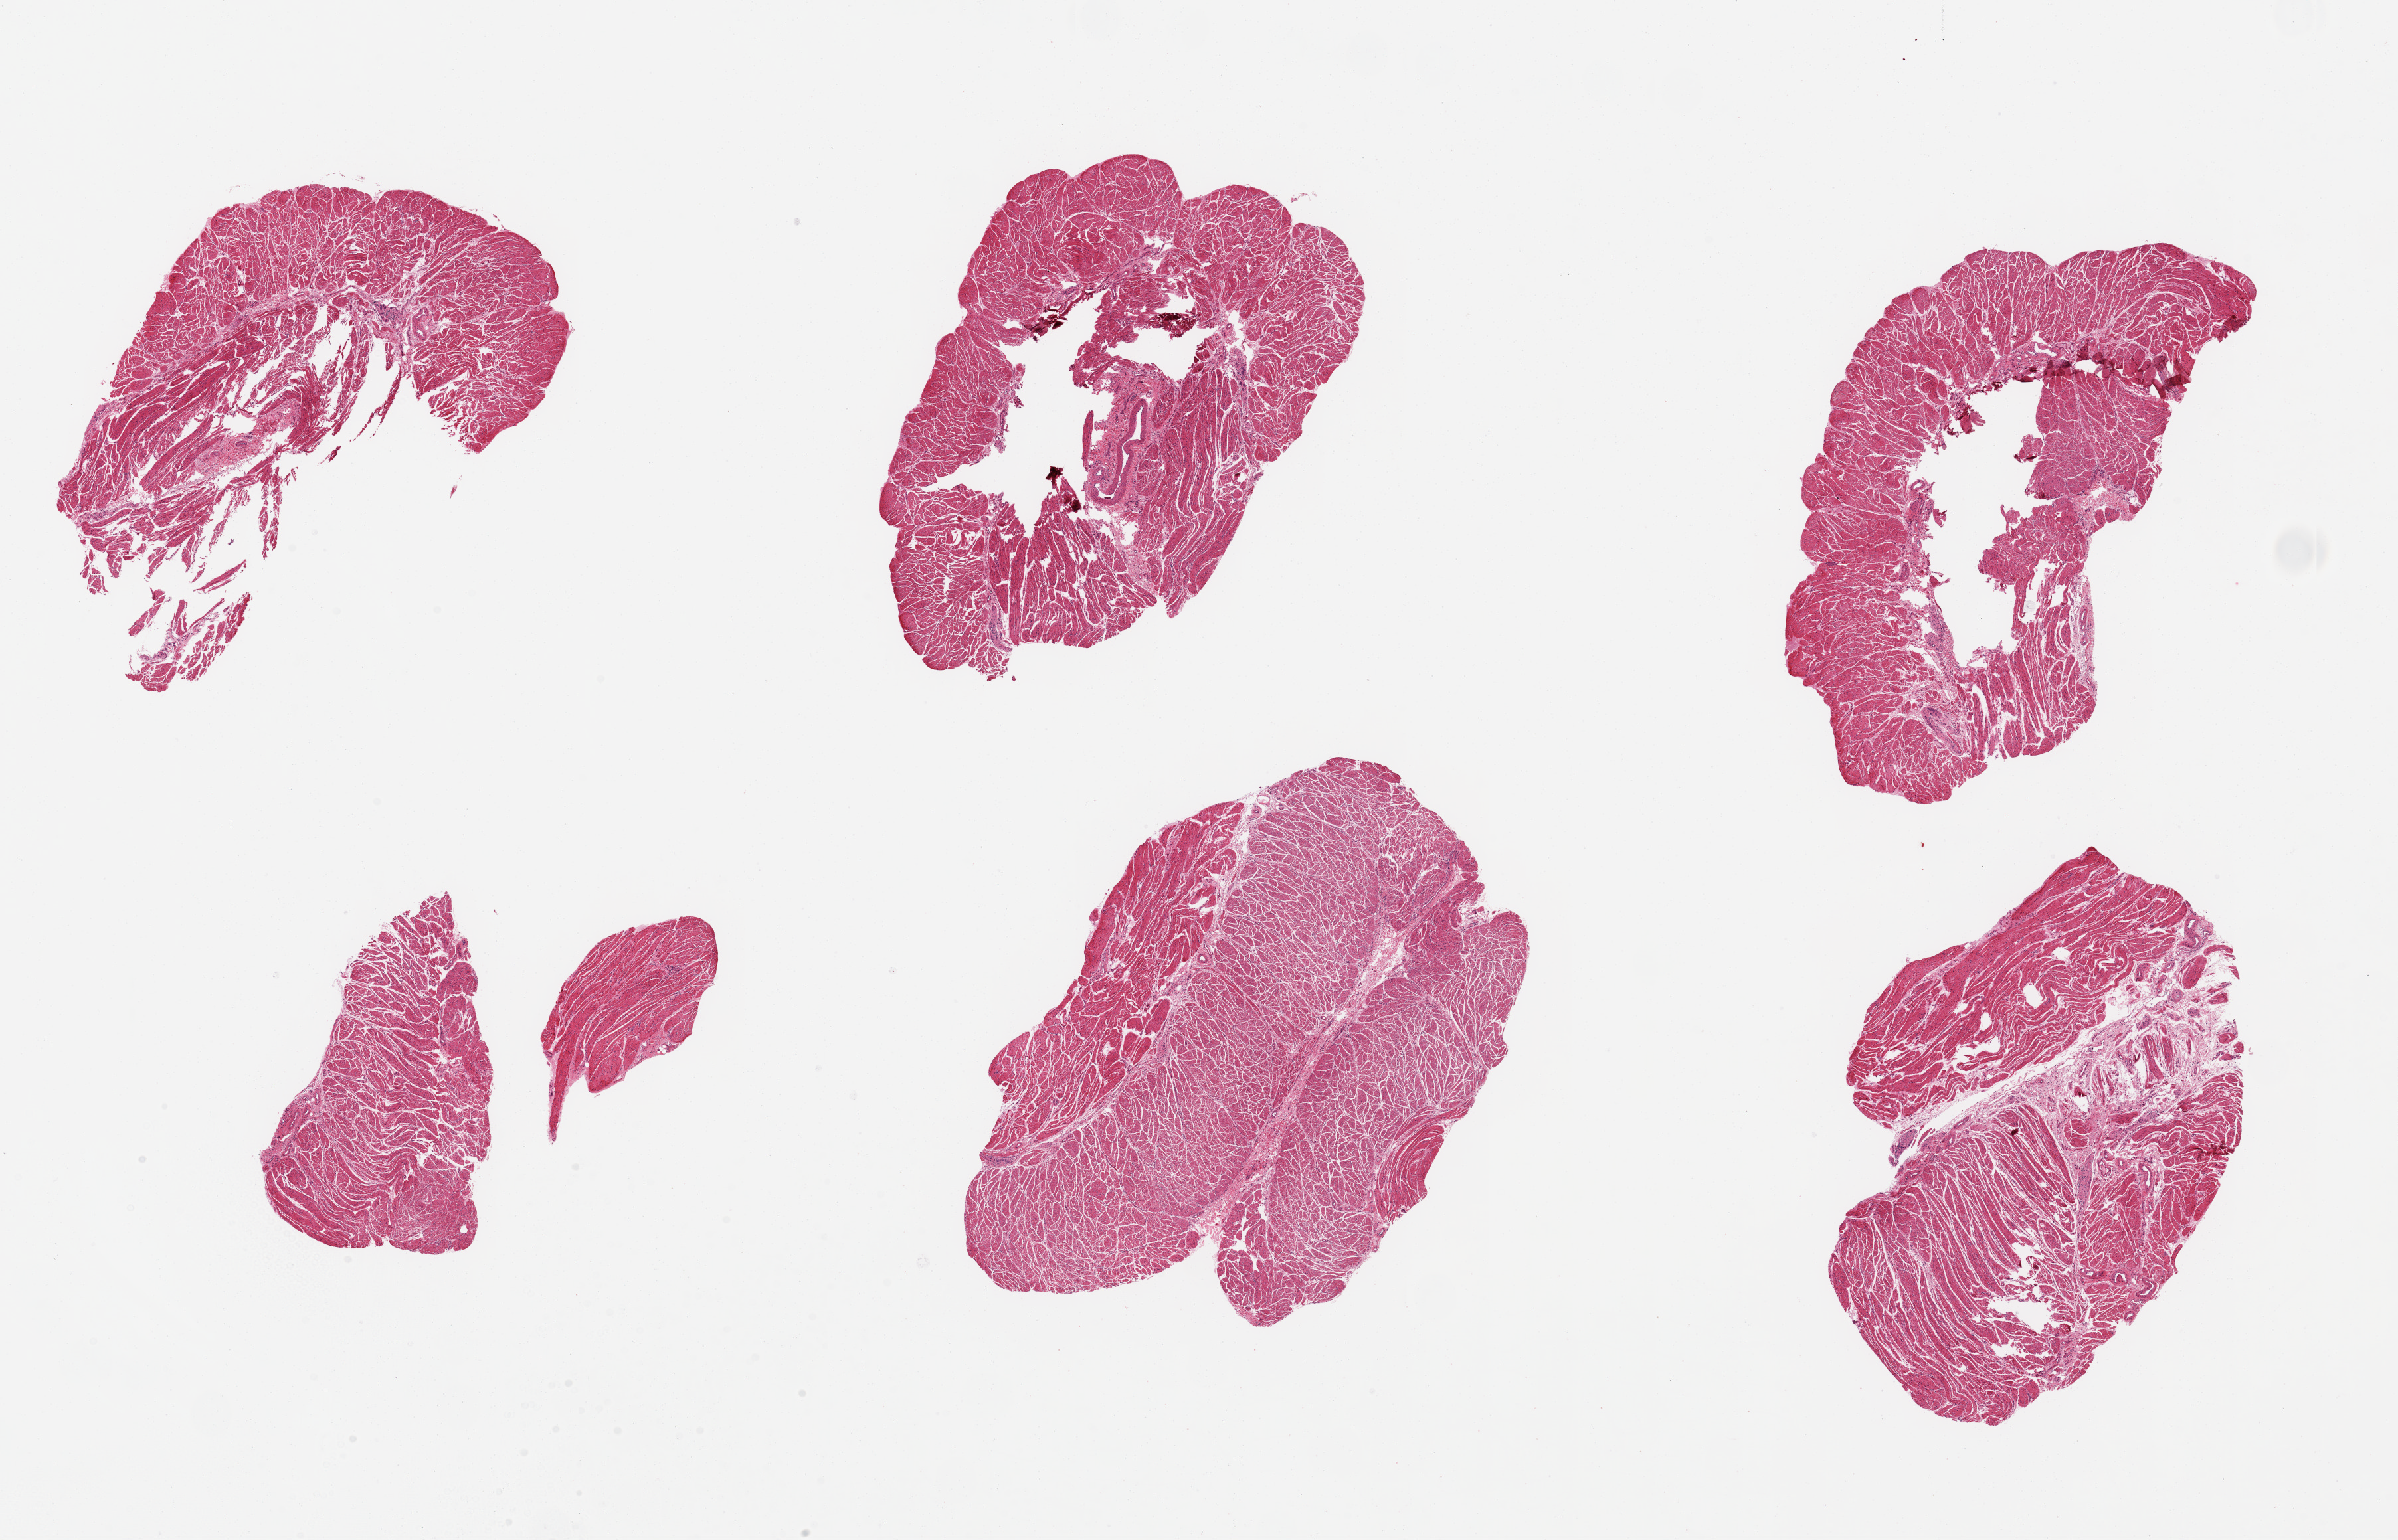
Hematoxylin and eosin (H&E) whole-slide image — low-resolution overview of the scanned area, about 28.5 x 18.3 mm, PAXgene-fixed paraffin-embedded (PFPE) section, sampled site (target tissue): esophageal muscle, donor tissue sample. Donor sex: male.
Reviewer comment on this tissue sample: 6 pieces, ~7x4mm.